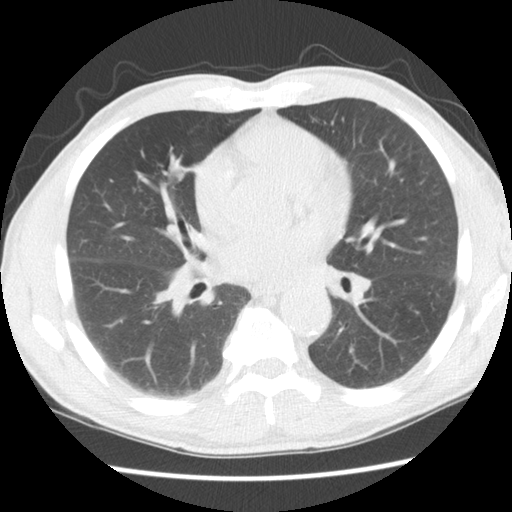
Chest CT (low-dose screening protocol), one axial image; second screening round (one year after baseline); lung window (W 1500 / L -600 HU); 2.5 mm slice thickness; slice 78 of 152 in the series. Male participant, aged 65 years at enrolment. Current smoker at enrolment.
Lesion marked by an expert reader, bounding box (x1, y1, x2, y2) in pixels: (129, 144, 200, 216). Reader record for this screening exam (exam-level; its link to the box is not recorded): non-calcified nodule or mass ≥4 mm, right middle lobe, 11 × 9 mm, smooth margins, soft tissue attenuation, pre-existing on the prior screen: no. Official screen result: positive, other. Participant outcome: lung cancer diagnosed 601 days after this screen (after the third annual screen) — squamous cell carcinoma, NOS, right middle lobe, poorly differentiated (G3), stage IA (AJCC 6th edition), 23 mm at pathology.